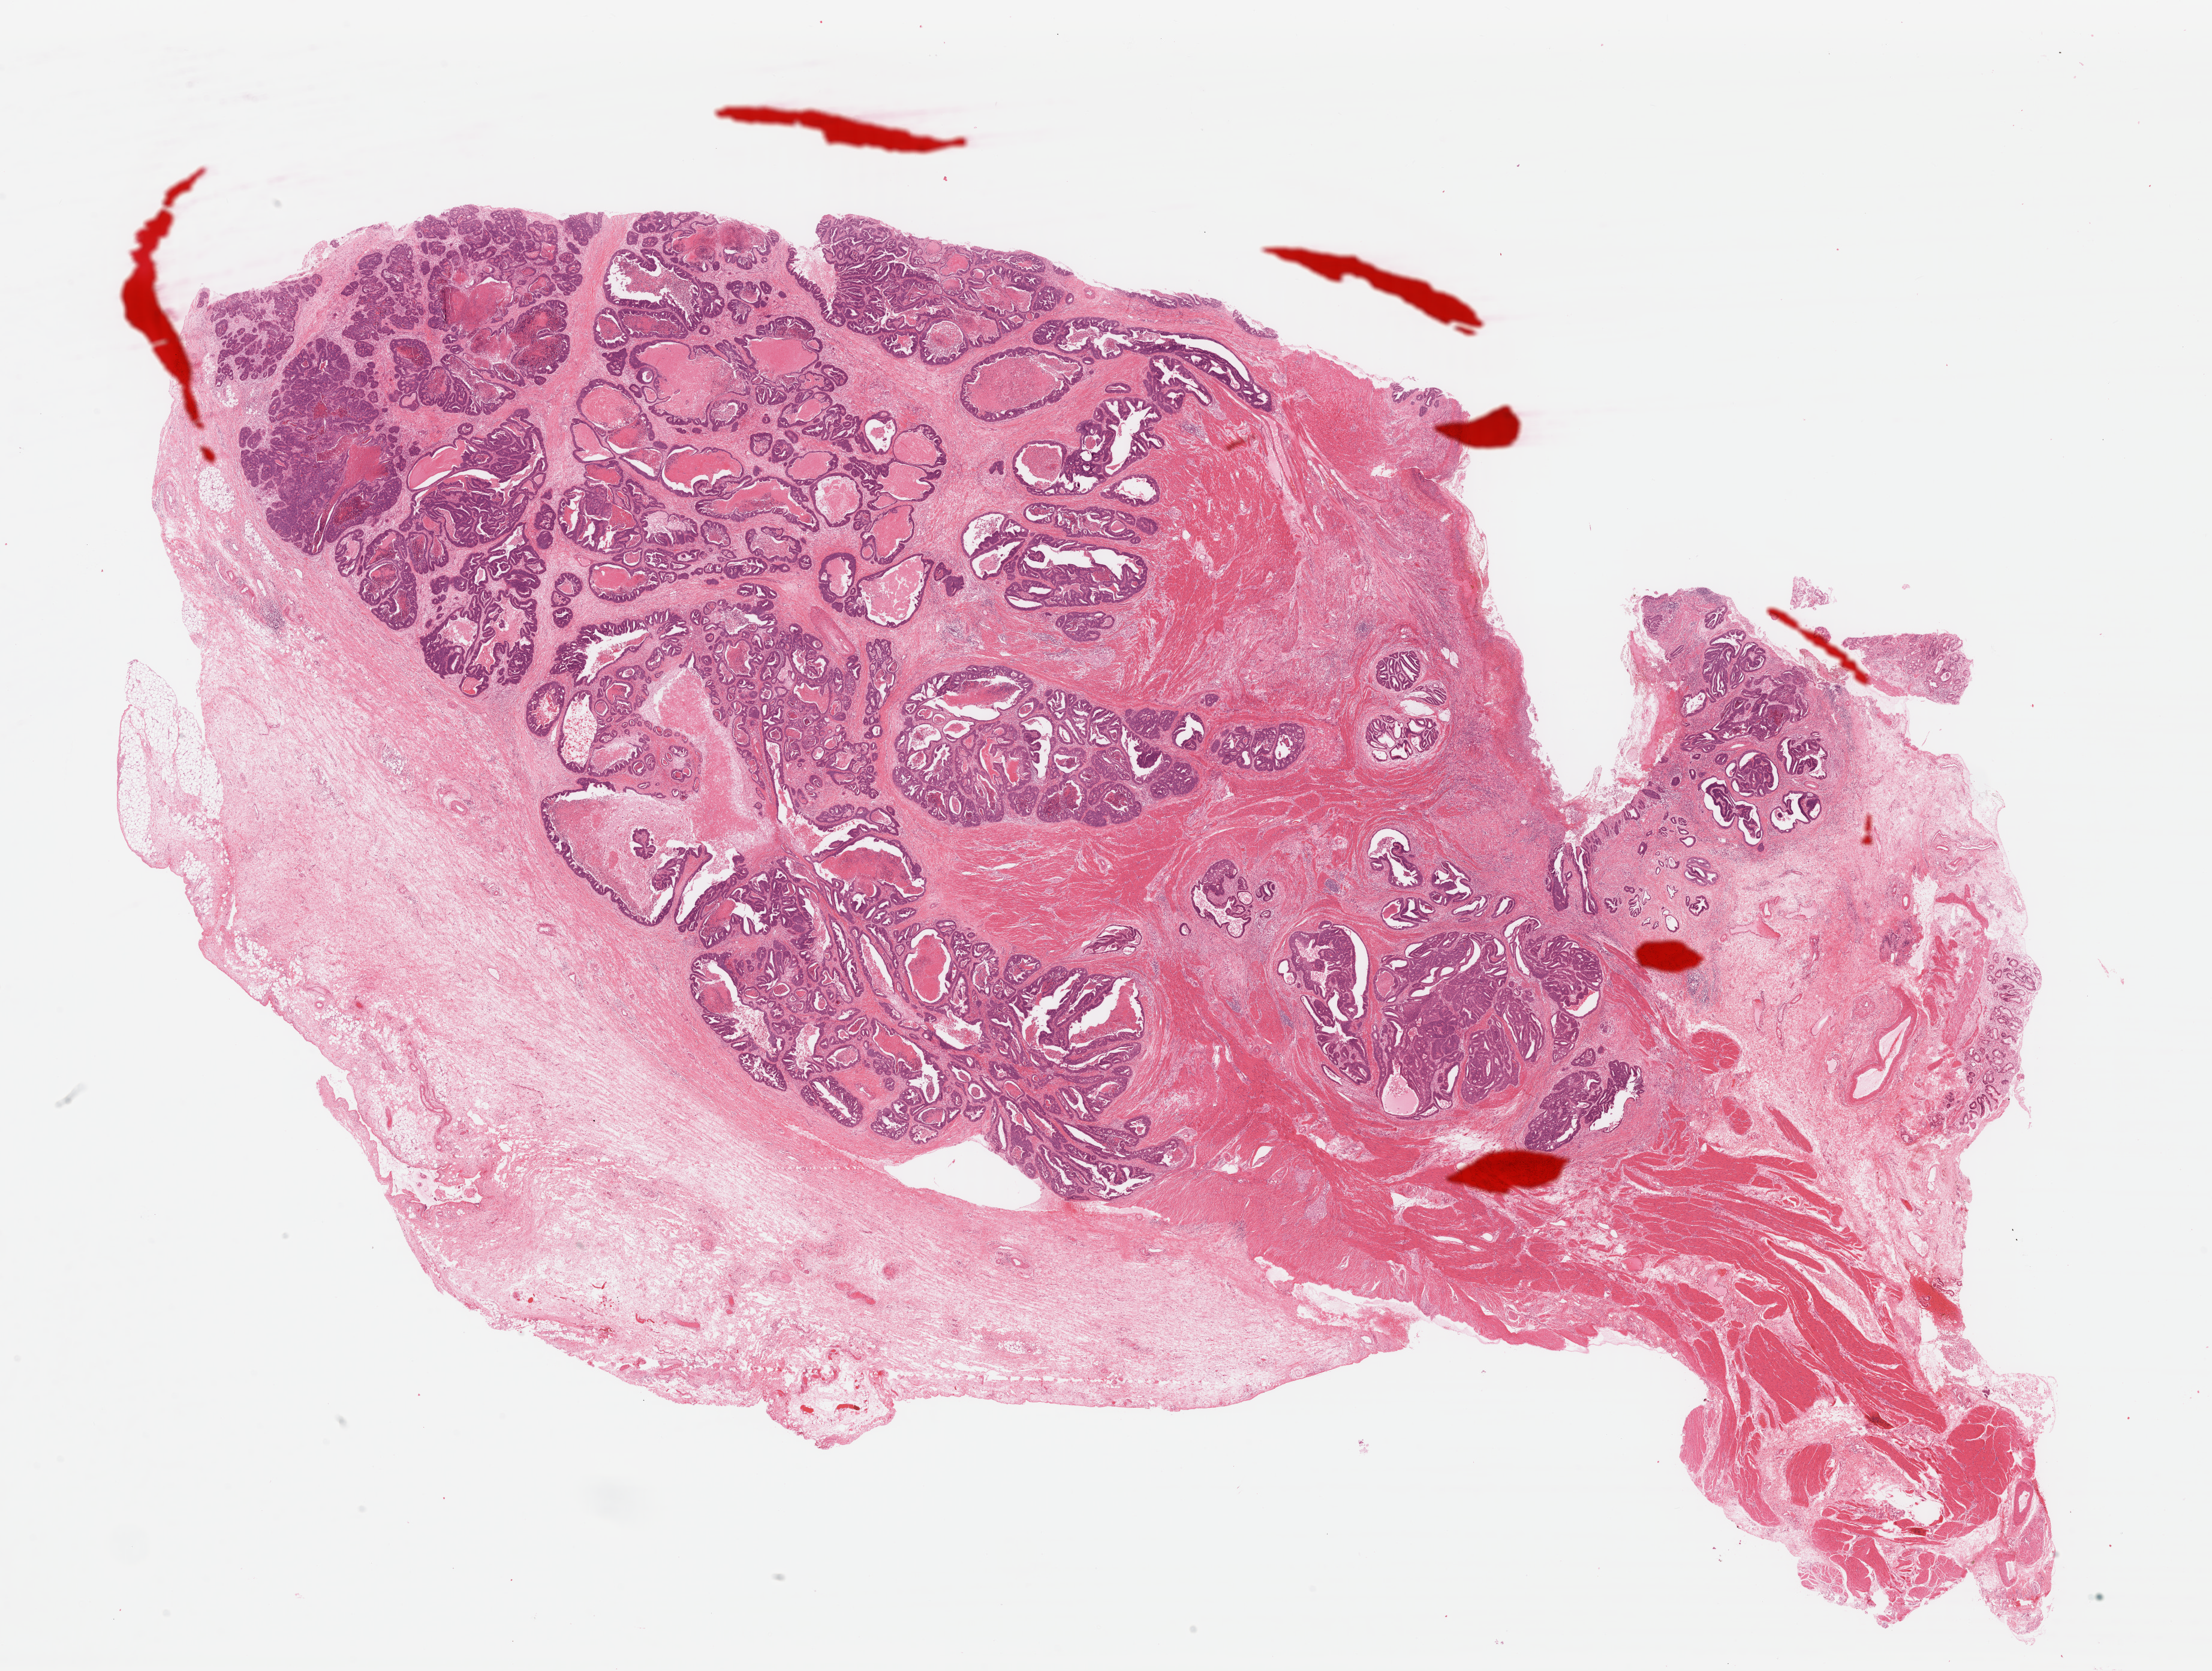
Digitized H&E-stained tissue section (whole slide), low-resolution overview of the scanned area, about 29.0 x 21.9 mm (slide scanned at 40x); formalin-fixed paraffin-embedded (FFPE) diagnostic section; stomach, primary tumour sample. Patient: male, age at initial diagnosis 57 years. Histologic grade: G3 (poorly differentiated).
Diagnosis: Tubular adenocarcinoma (gastric antrum). AJCC pathologic stage: IIIA. Lymph nodes positive (case pathology): 2 of 4 examined.